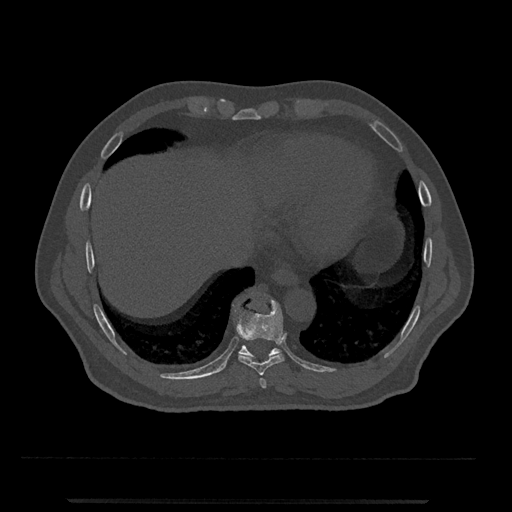
CT including the spine, one axial slice; slice 555 of 797 in the series (ordered by position); 120 kVp; bone window (W 1800 / L 400 HU); 0.5 mm slice thickness; 512 × 512 image matrix. Patient: male, 63 years. Case-level facts recorded for this patient, not image findings: primary cancer: prostate.
Structures marked on this image (semi-automatic segmentation, software-assisted and operator-edited):
- T10 vertebra: box from (x=233, y=304) to (x=282, y=357) px
- T8 vertebra: (x=259, y=378)–(x=267, y=388)
- T9 vertebra: (x=236, y=299)–(x=285, y=375)